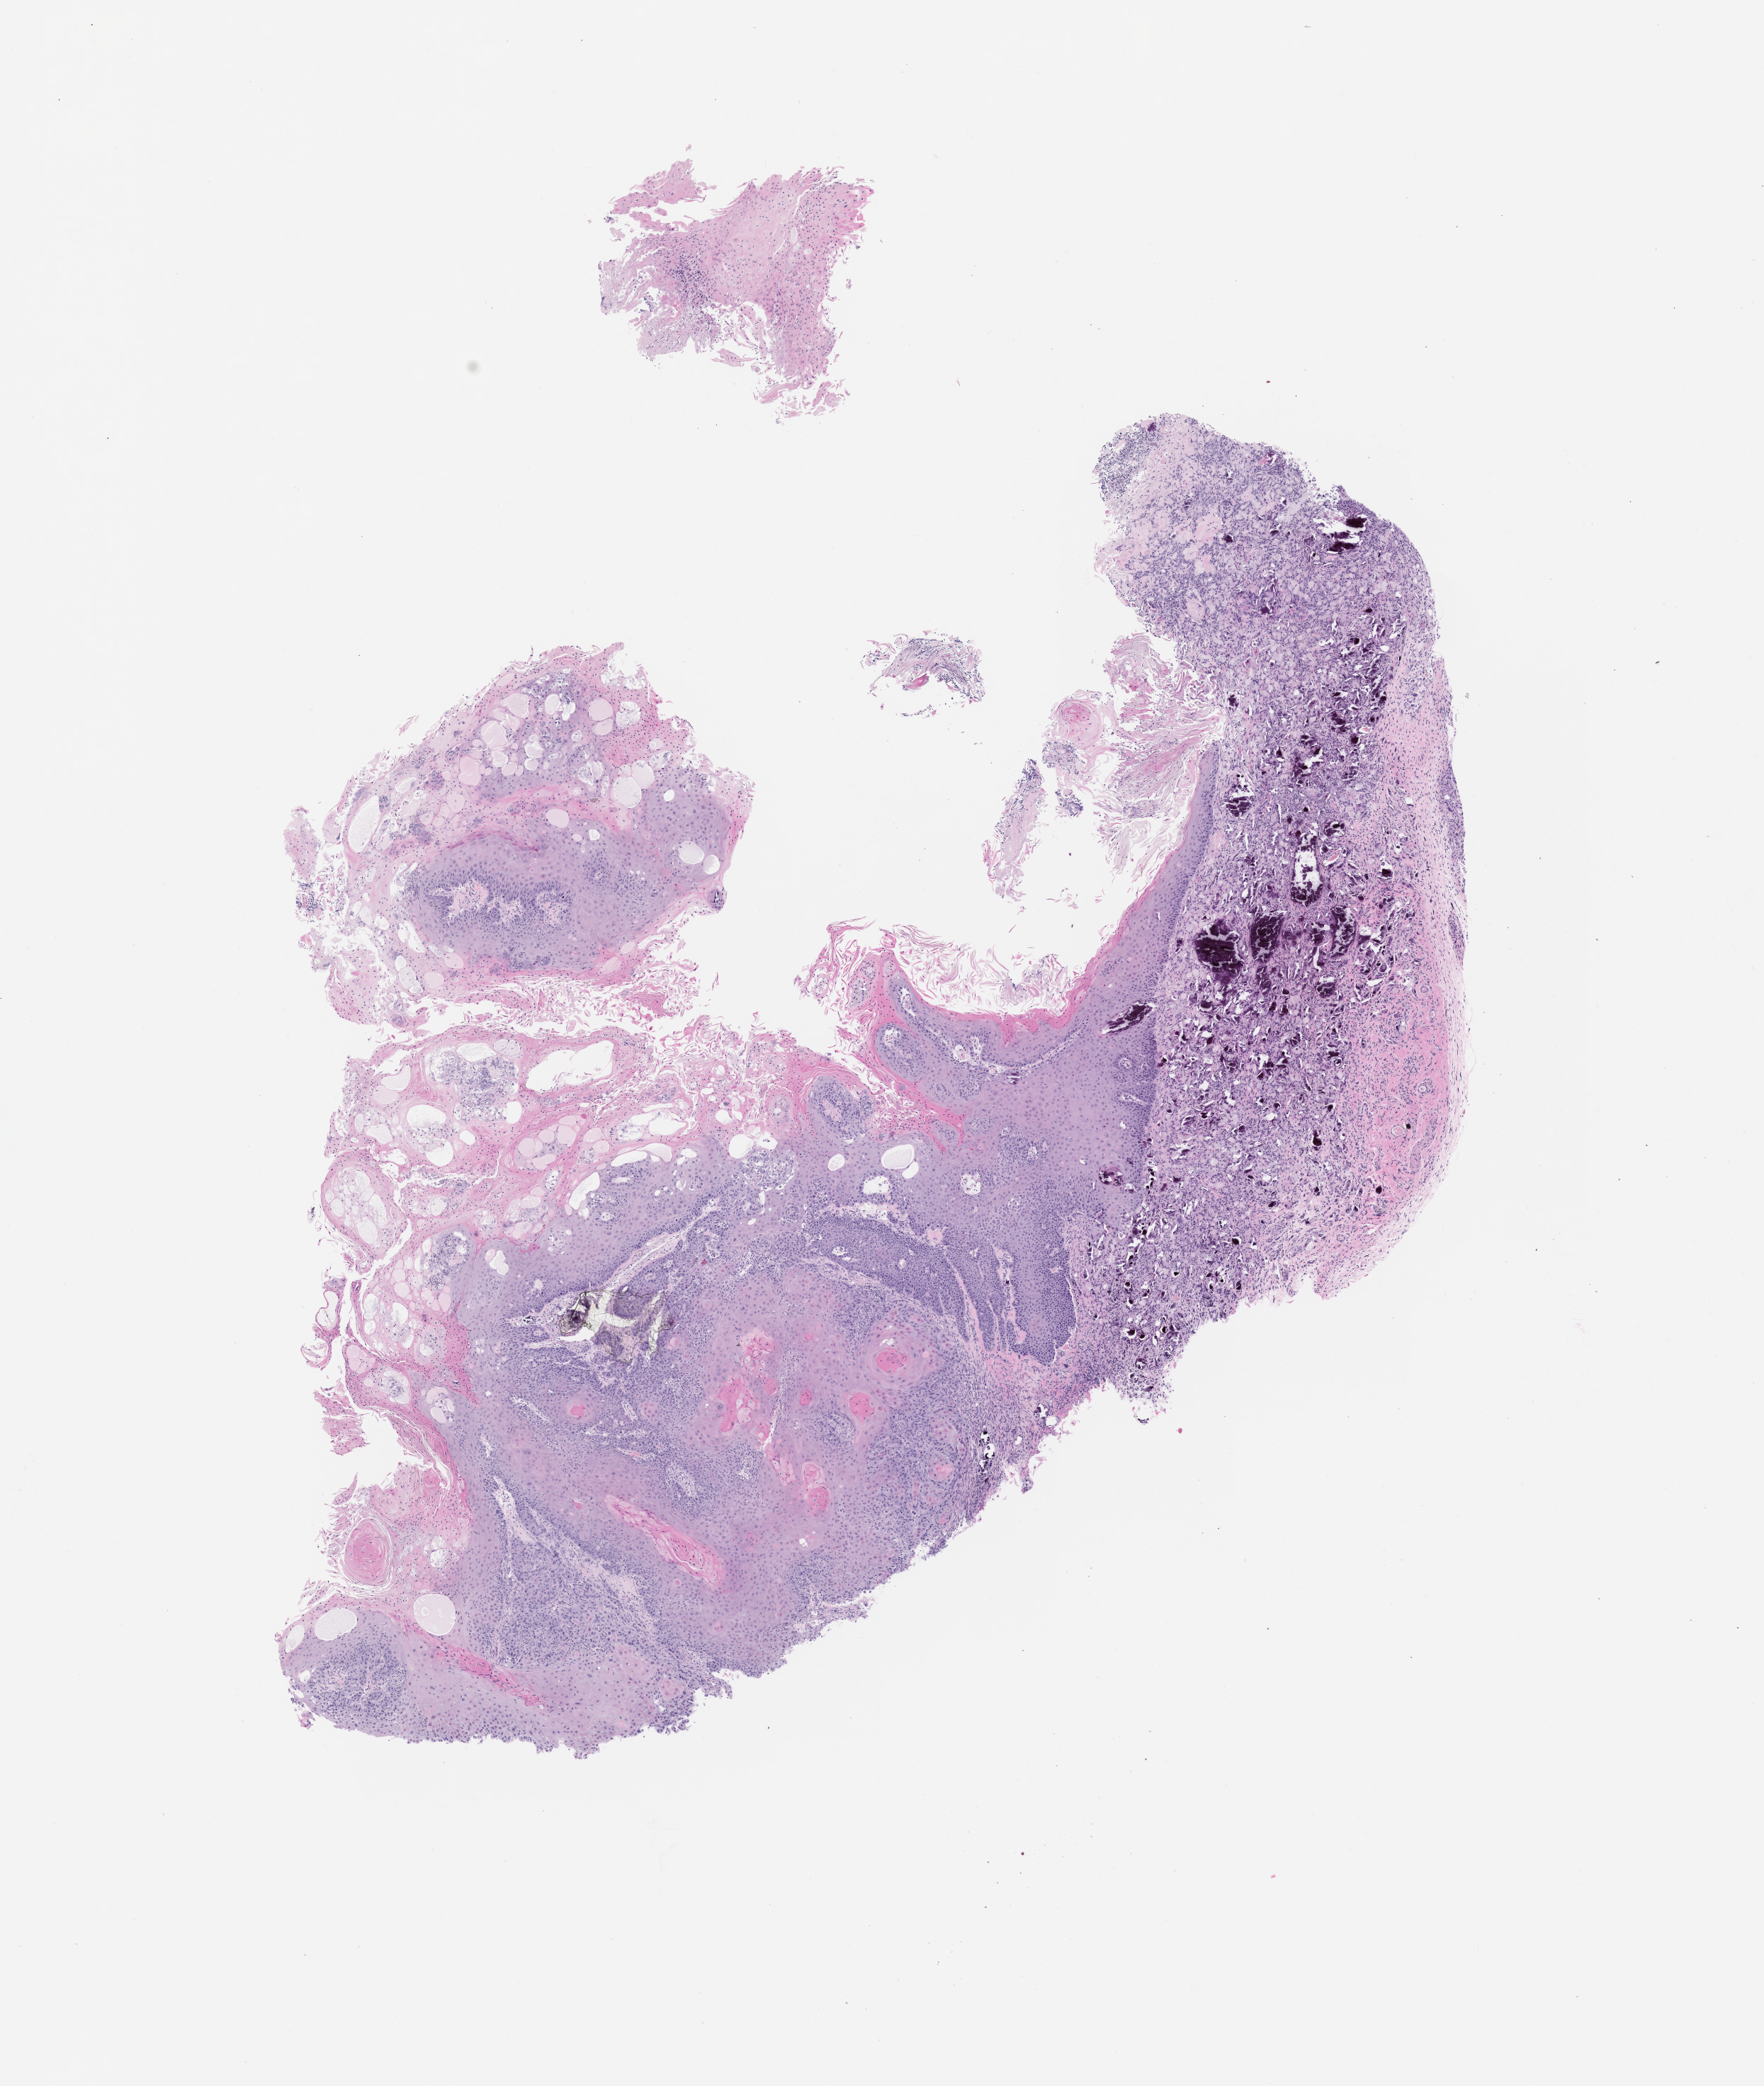
Hematoxylin and eosin (H&E) whole-slide image of a patient-derived xenograft (PDX) tumor grown in a mouse, passage 1 — whole scanned area (about 10.0 x 11.8 mm) shown as a low-resolution overview. Formalin-fixed, paraffin-embedded (FFPE) tissue. Tumor site category: oral soft tissue.
Originating patient diagnosis: Head and Neck Squamous Cell Carcinoma.